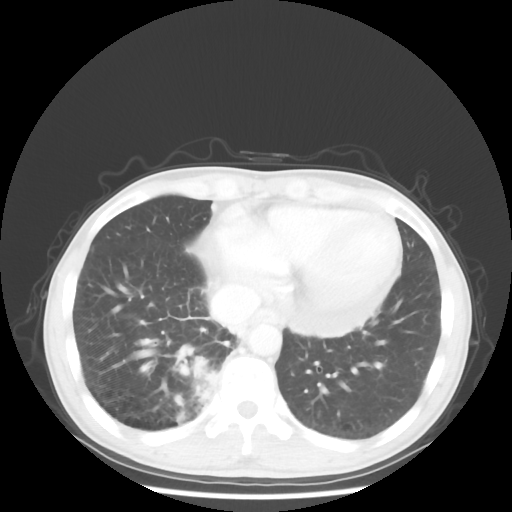
Chest CT, one axial slice. Slice 14 of 58 in the series (ordered by position). Reconstruction kernel STANDARD. 100 kVp. Lung window (W 1500 / L -600 HU). 5 mm slice thickness. 512 × 512 image matrix. Patient: male, 56 years. From the clinical record (not read from this slice): clinical TNM (as recorded): T2 N1 M1; histopathological grade: G1.
Outlined on this slice (rectangle marked by the reading radiologist):
- lung tumour (recorded histology: adenocarcinoma): bounding box <189,355,218,401> (left, top, right, bottom; pixels)